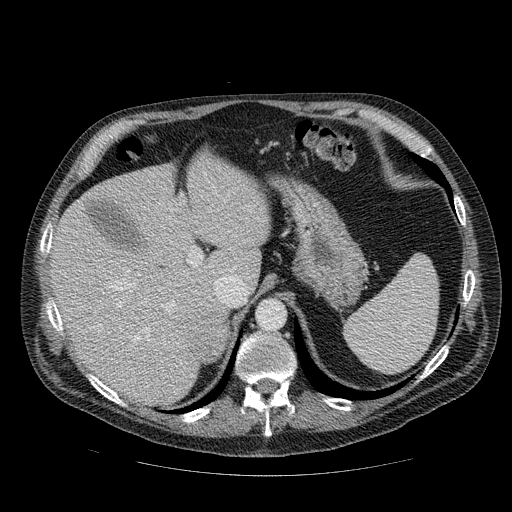
Contrast-enhanced abdominal CT, one axial slice; slice 70 of 111 in the series (ordered by position); reconstruction kernel STANDARD; 120 kVp; intravenous contrast given; soft-tissue window (W 400 / L 40 HU); 2.5 mm slice thickness; 512 × 512 image matrix. Male patient, age 56 years. From the clinical record (not read from this slice): diagnosis: adrenocortical carcinoma; tumour side: right adrenal.
Outlined on this slice (semi-automatically segmented with operator editing):
- mass: bounding box <190,319,228,362> (left, top, right, bottom; pixels)